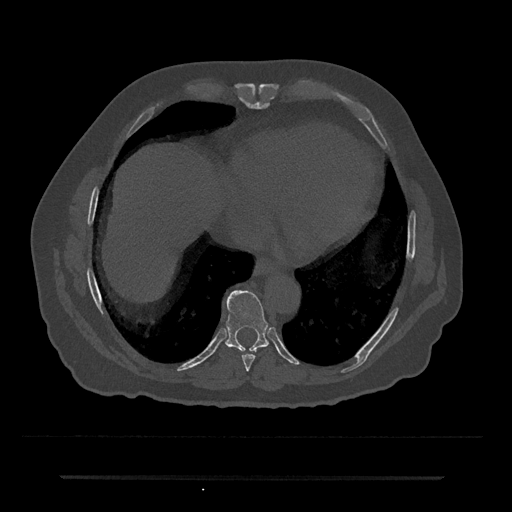
CT including the spine, one axial slice. Position 297 of 797 along the scan axis. Reconstruction kernel Br40s/3. 120 kVp. Bone window (W 1800 / L 400 HU). 0.5 mm slice thickness. 512 × 512 image matrix, field of view 437 × 437 mm. Patient: male, 69 years. Case-level facts recorded for this patient, not image findings: primary cancer: prostate.
Annotated regions visible in this slice (semi-automatically segmented with operator editing):
- T8 vertebra: box from (x=242, y=354) to (x=256, y=371) px
- T9 vertebra: (x=225, y=290)–(x=269, y=352)